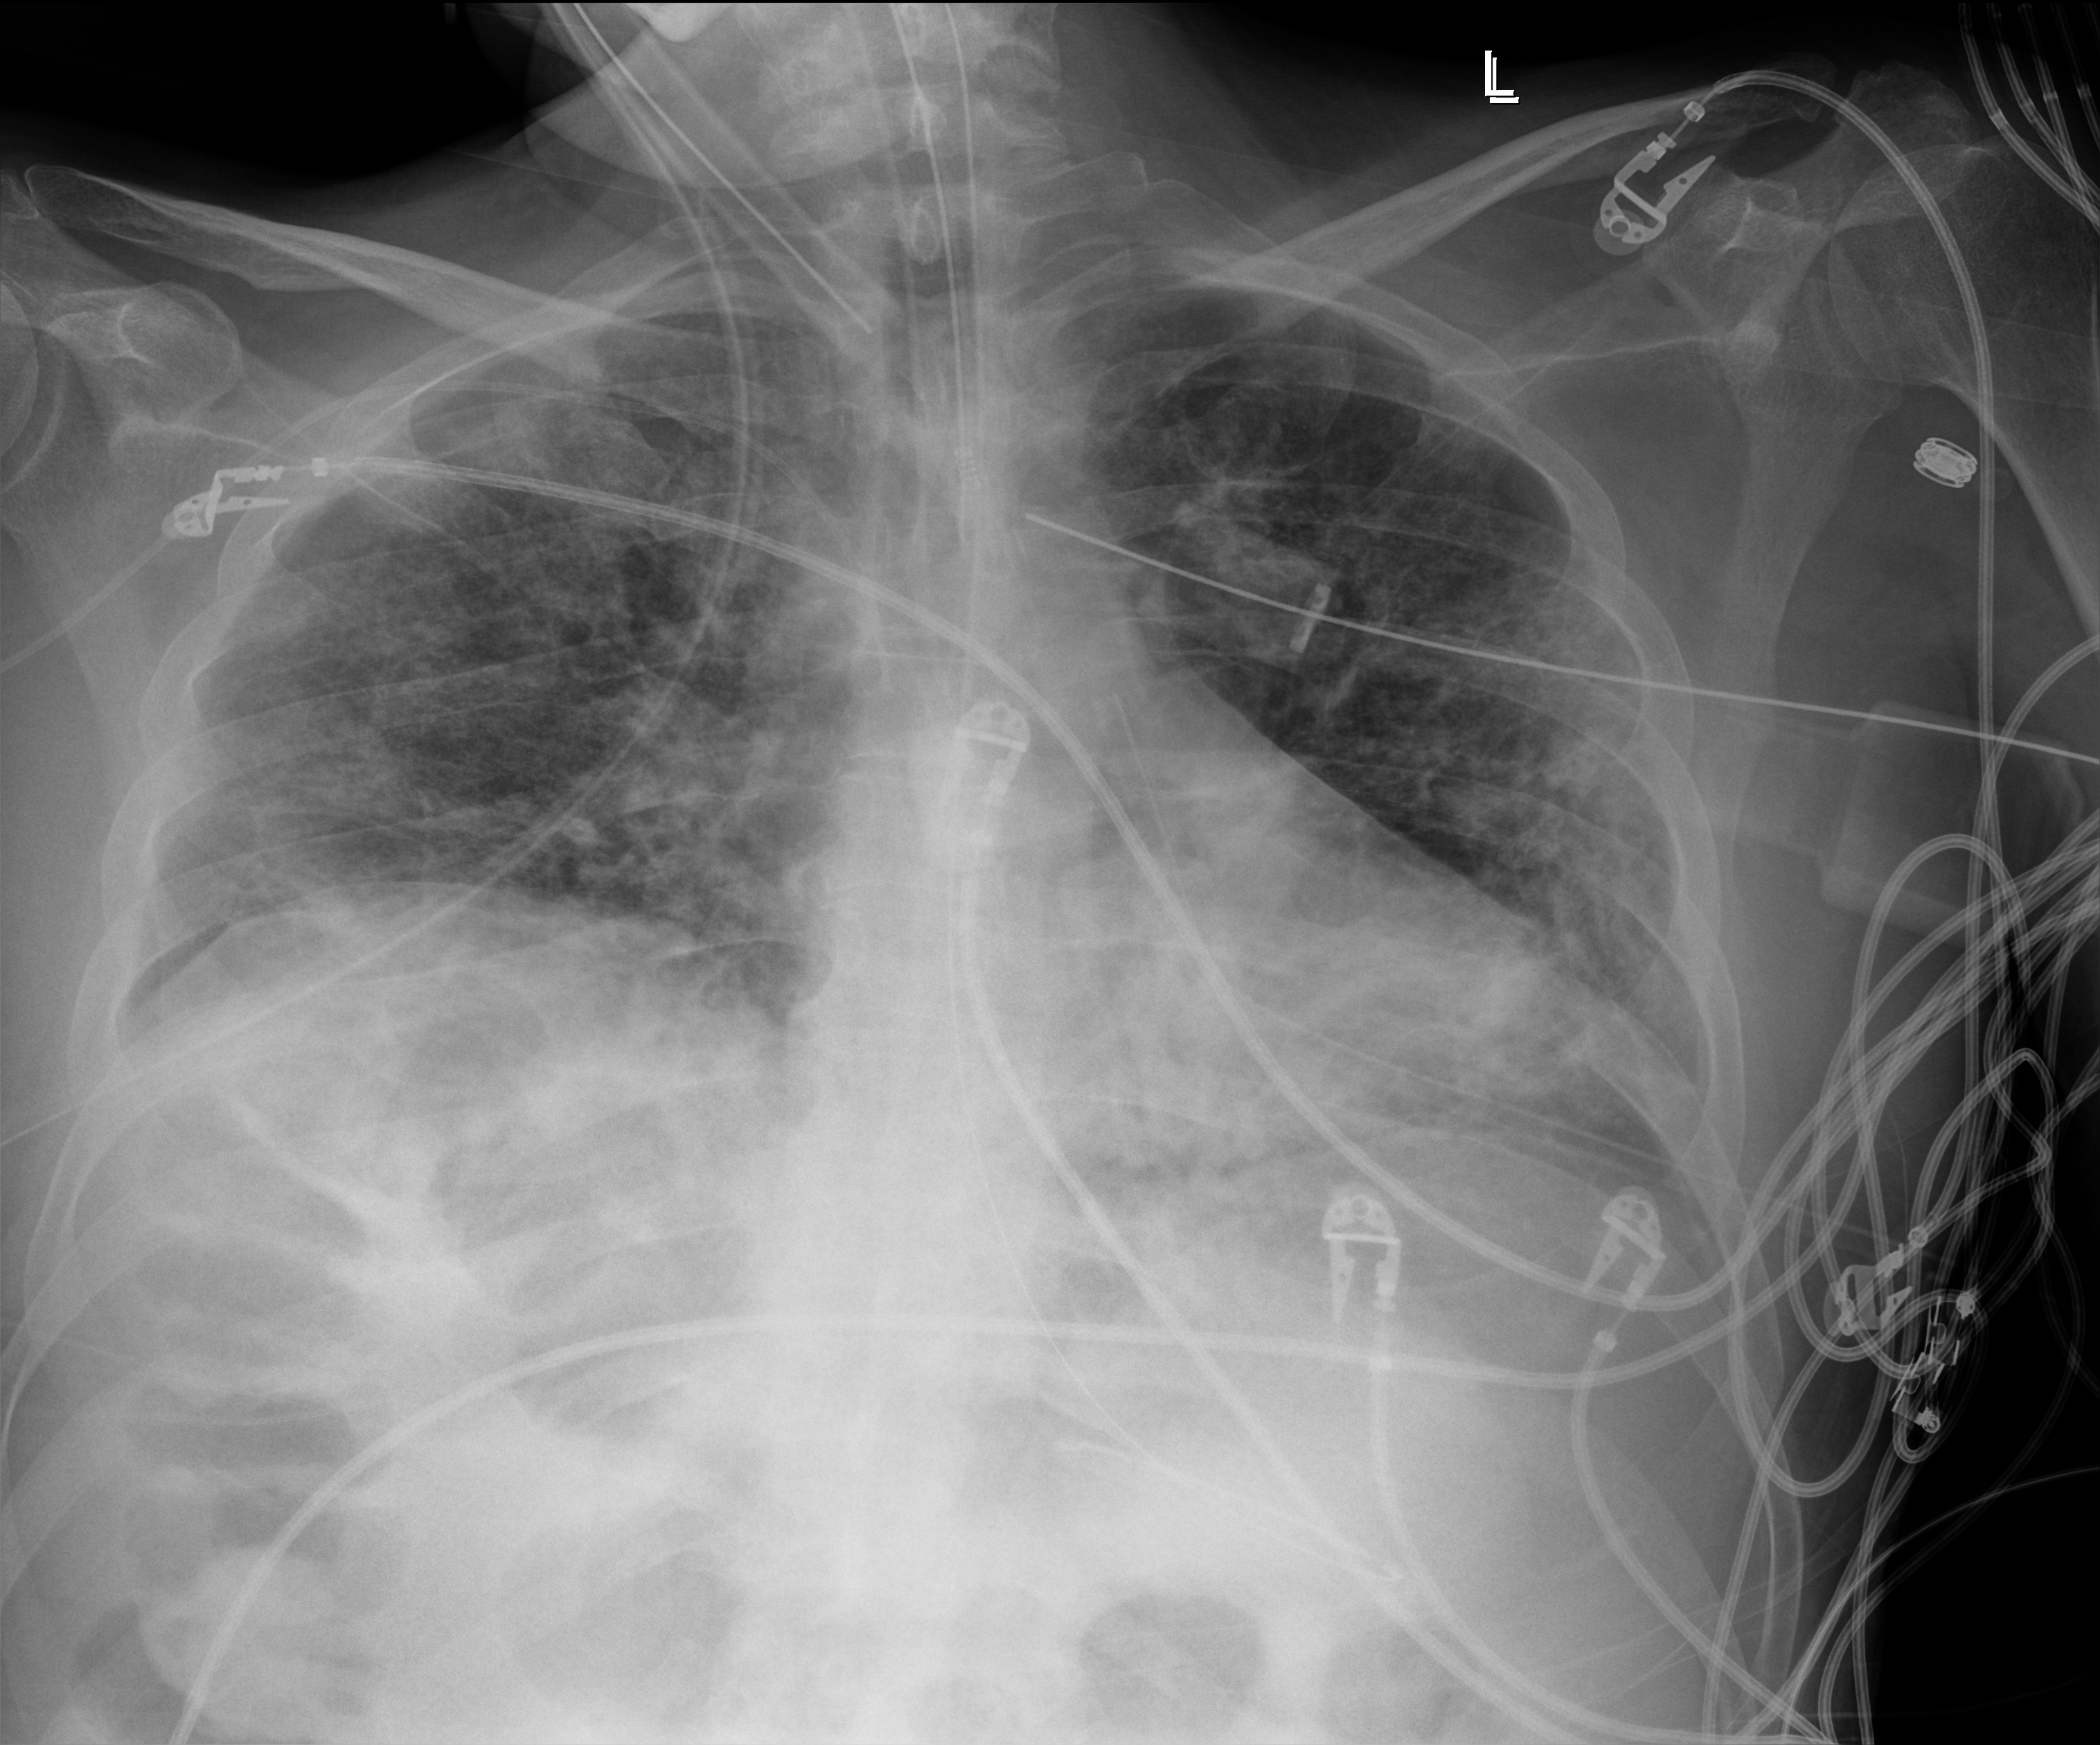
Portable chest radiograph. Patient hospitalised with COVID-19; male, aged 18–59 years.
Admission-level facts for this patient (not findings on this image; timing relative to this image not recorded): admitted to intensive care during this hospital stay: yes; mechanically ventilated during this hospital stay: yes; diabetes (admission record): no.